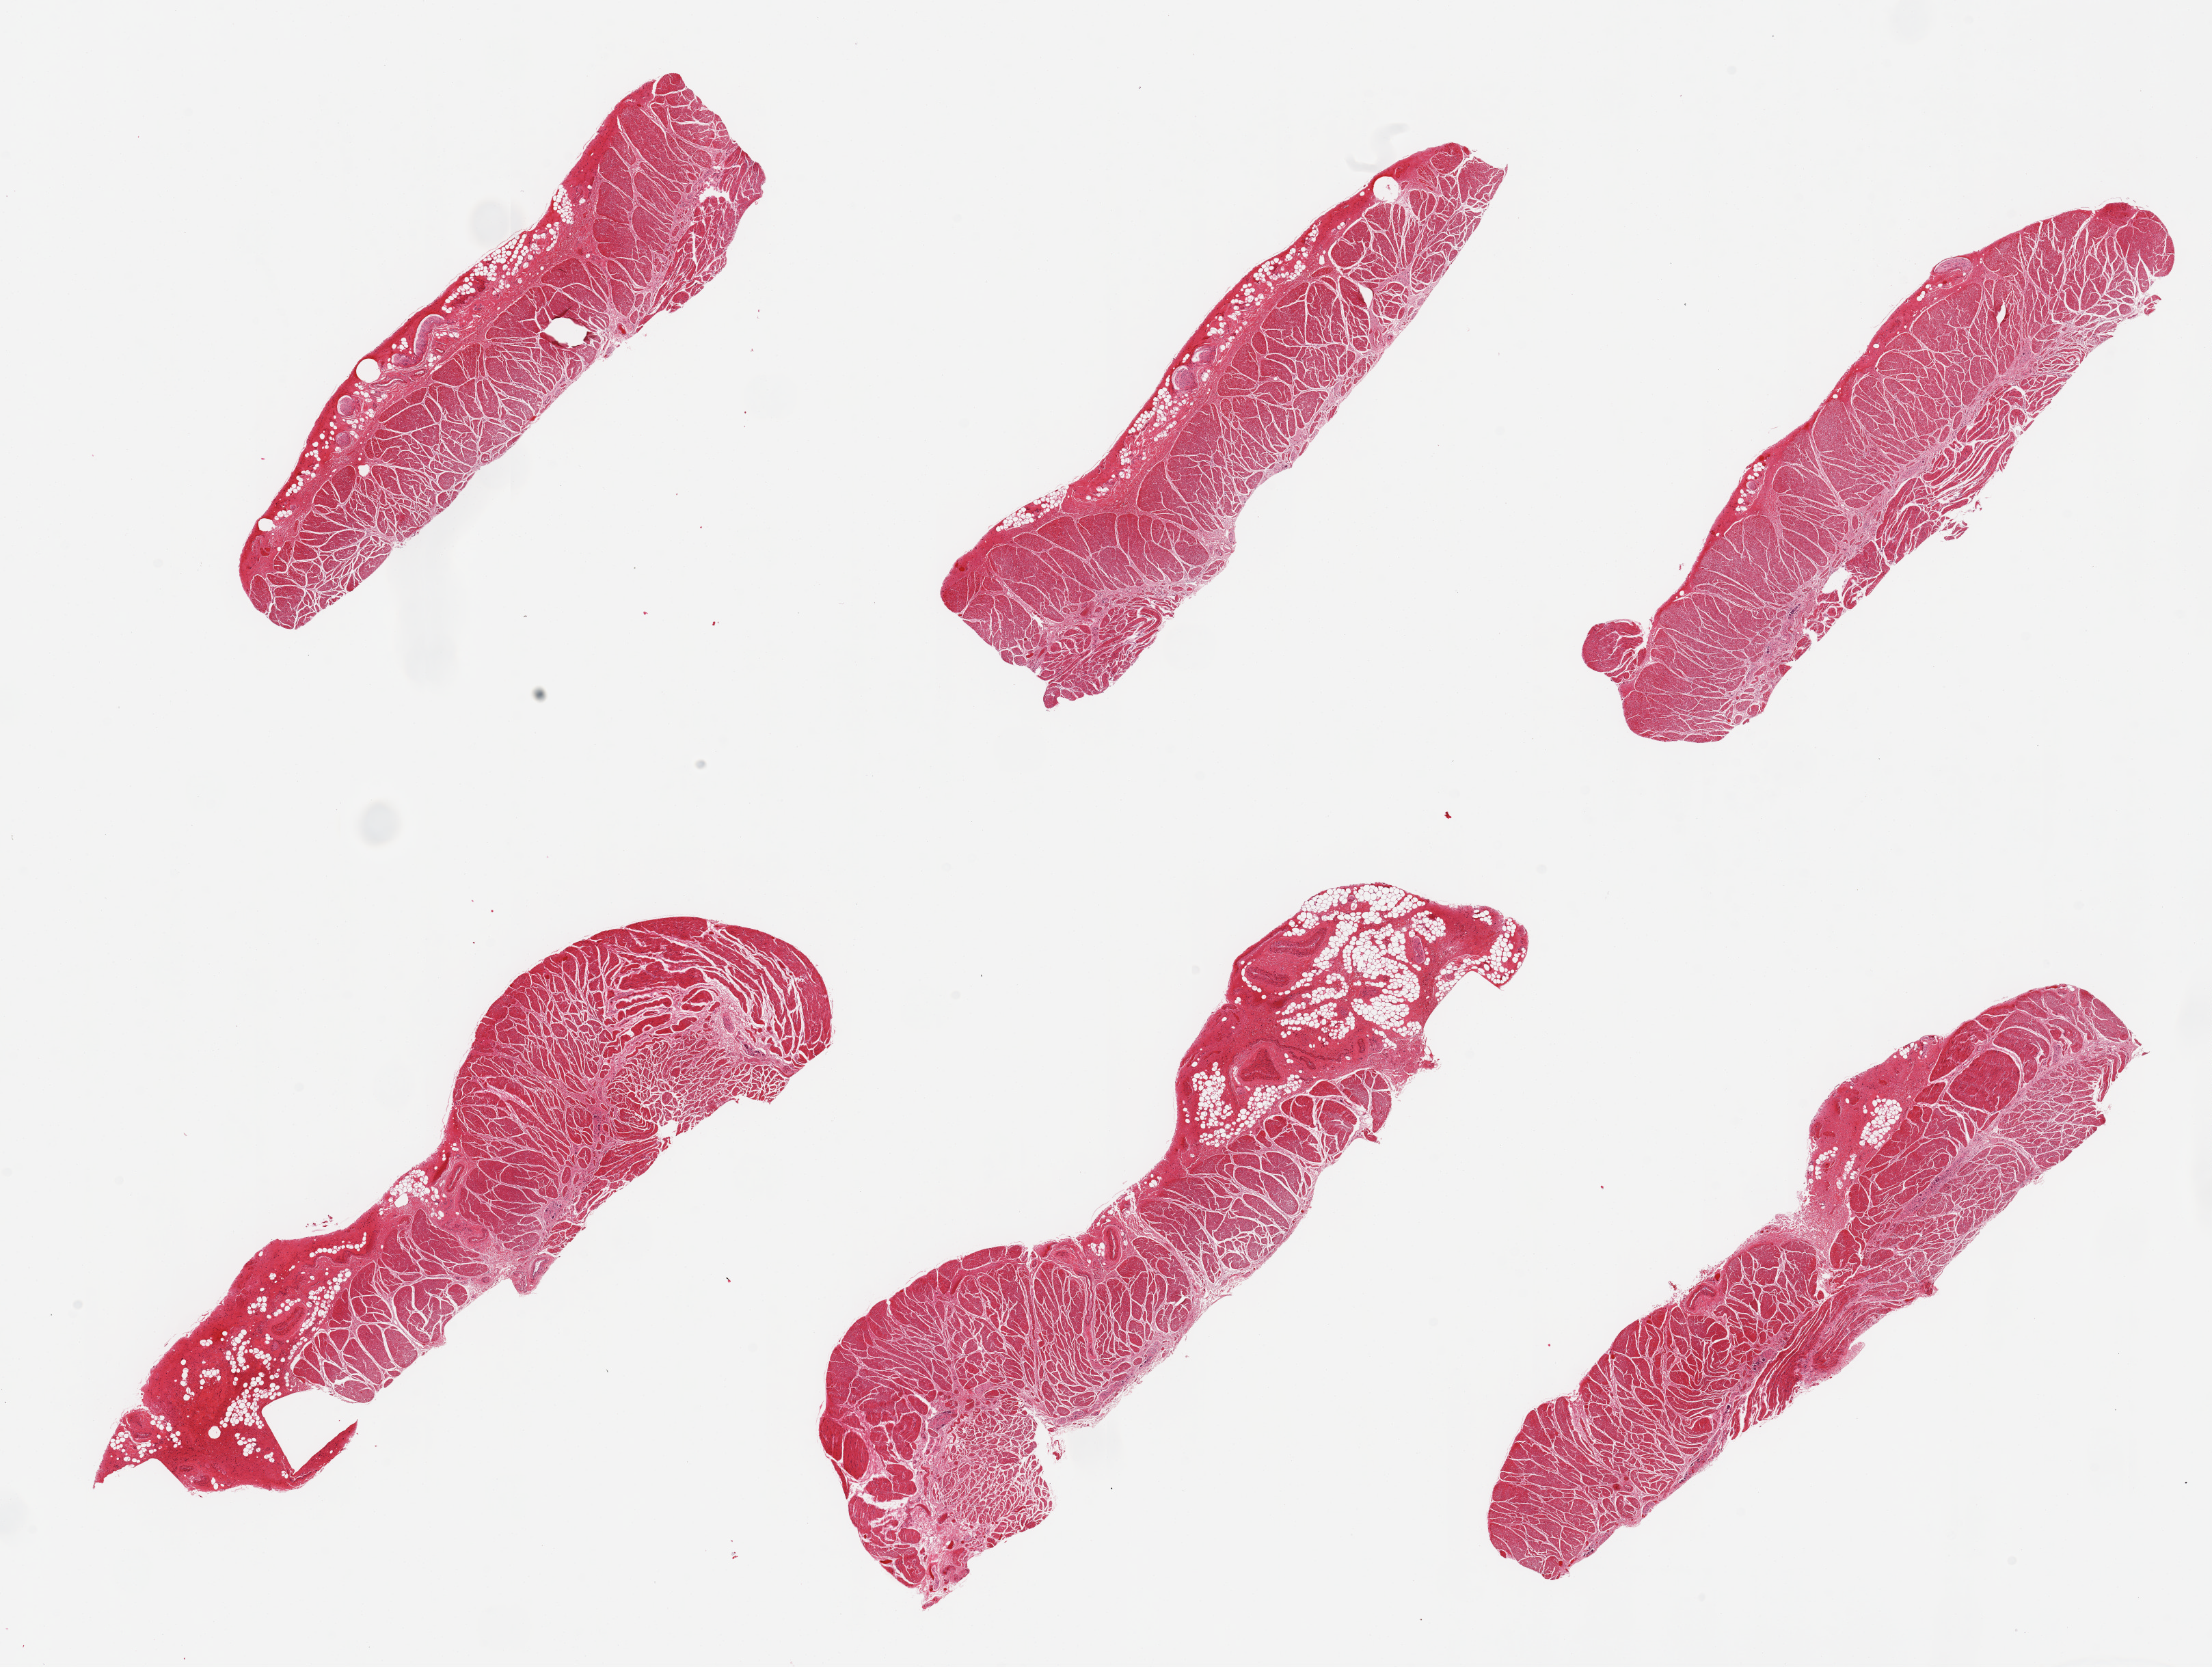
Digitized haematoxylin and eosin-stained section, brightfield — shown as a low-resolution overview of the whole scanned area (about 25.6 x 19.3 mm, acquisition: 20x scan), PAXgene-fixed paraffin-embedded (PFPE) section, target tissue: esophageal muscle, tissue donor sample. Donor: male.
Reviewer comment on this tissue sample: 6 pieces; up to 20% of attached fat, nerve, and vessels.